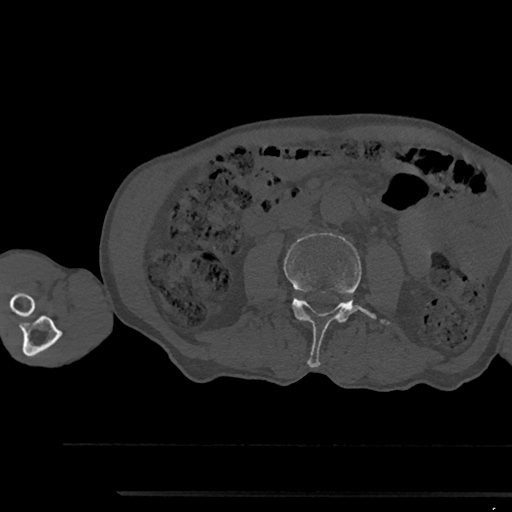
CT including the spine, one axial slice; slice 483 of 797 in the series (ordered by position); reconstruction kernel Br40s/3; bone window (W 1800 / L 400 HU); 512 × 512 image matrix. Patient: male, 79 years. Case-level facts recorded for this patient, not image findings: primary cancer: prostate.
Outlined on this slice (semi-automatic segmentation, software-assisted and operator-edited):
- L3 vertebra: bounding box (x1, y1, x2, y2) in pixels: (284, 233, 389, 367)